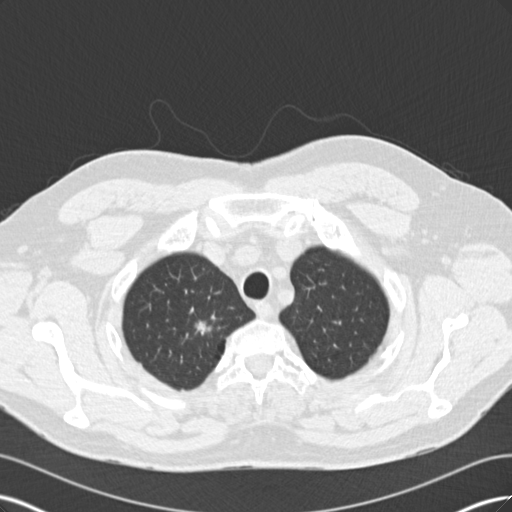
Low-dose screening chest CT, one axial slice; slice 150 of 171 in the series (ordered by position); reconstruction kernel B30f; lung window (W 1500 / L -600 HU); 2 mm slice thickness; 512 × 512 image matrix.
Structures marked on this image (outlined manually by an expert reader):
- lesion 1 (tumor, upper lobe of right lung): bounding box <195,321,212,335> (left, top, right, bottom; pixels)